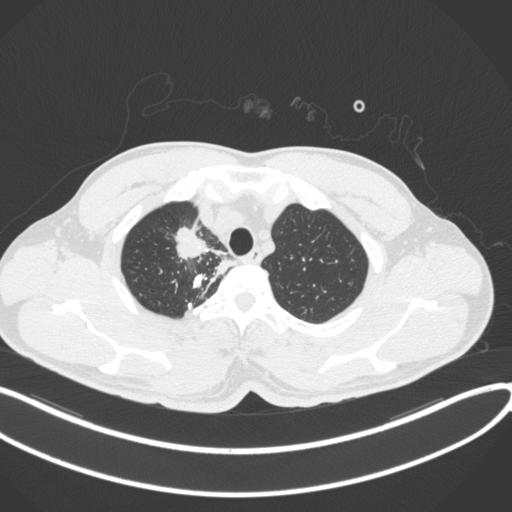
Chest CT, one axial slice; slice 324 of 391 in the series (ordered by position); reconstruction kernel B31f; 120 kVp; lung window (W 1500 / L -600 HU); 1 mm slice thickness; 512 × 512 image matrix. Male patient, age 48 years. Case-level facts recorded for this patient, not image findings: clinical TNM (as recorded): T1c N1 M1.
Annotated regions visible in this slice (rectangle marked by the reading radiologist):
- lung tumour (recorded histology: adenocarcinoma): bounding box (x1, y1, x2, y2) in pixels: (168, 219, 211, 259)